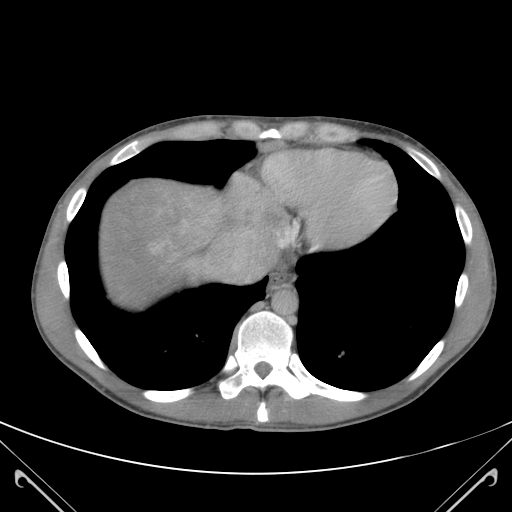
Contrast-enhanced abdominal CT (liver protocol), one axial slice; position 107 of 118 along the scan axis; soft-tissue window (W 400 / L 40 HU); 3 mm slice thickness; 512 × 512 image matrix, field of view 380 × 380 mm. From the clinical record (not read from this slice): diagnosis: hepatocellular carcinoma (patient treated with transarterial chemoembolisation; whether this scan precedes or follows treatment is not stated here); TNM stage (as recorded): Stage-IIIB; Child-Pugh class: A.
Outlined on this slice (semi-automatically segmented with operator editing):
- abdominal aorta: bounding box (x1, y1, x2, y2) in pixels: (273, 291, 297, 314)
- liver parenchyma outside the tumour (the mass and vessels are separate outlines, so this box may not span the whole liver): (100, 180, 236, 298)